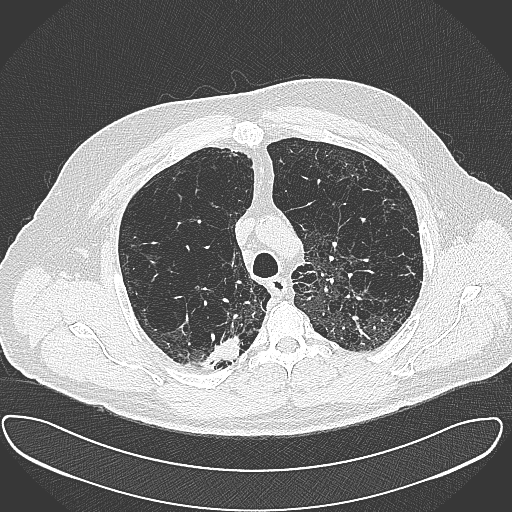
Chest CT (low-dose screening protocol), one axial image. First (baseline) screen. Lung window (W 1500 / L -600 HU). 1 mm slice thickness. Lung (sharp) reconstruction kernel (B80f). 512 × 512 image matrix, field of view 408 × 408 mm. Male, age 60 years at enrolment.
- Expert-annotated lung lesion, bounding box (x1, y1, x2, y2) in pixels: (196, 327, 247, 373).
- Screening reader's record for this exam (one nodule recorded; not confirmed to be the boxed lesion): non-calcified nodule or mass ≥4 mm, right upper lobe, 15 × 25 mm, spiculated (stellate) margins, soft tissue attenuation.
- Official screen result: positive, change unspecified: nodule(s) >= 4 mm or enlarging nodule(s), mass(es), or other non-specific abnormalities suspicious for lung cancer.
- Participant outcome: lung cancer diagnosed 32 days after this screen — carcinoma, NOS, right upper lobe, moderately differentiated (G2), stage IB (AJCC 6th edition), 35 mm at pathology.